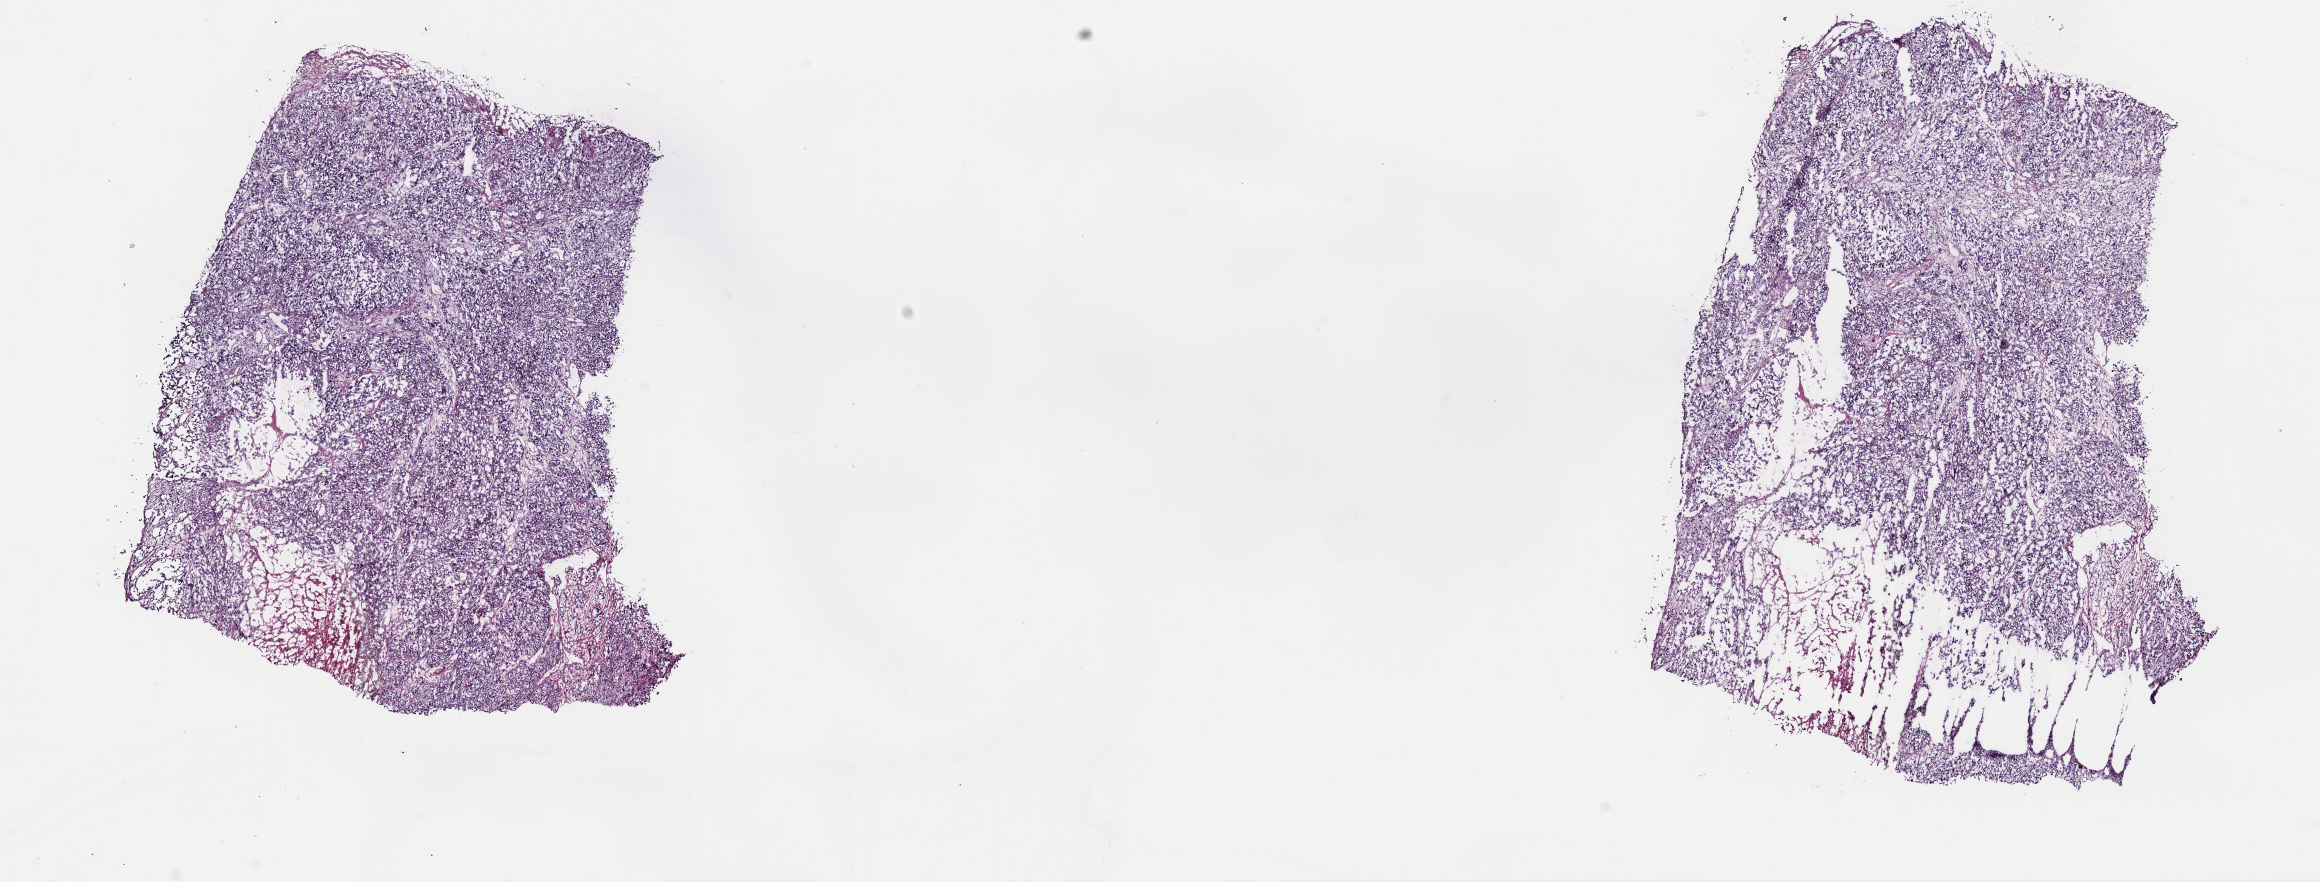
Whole-slide histology image, H&E-stained — low-resolution overview of the scanned area, about 18.3 x 7.0 mm (slide scanned at 40x), frozen section from the top of the tissue portion, primary tumour sample from the skin. Female patient; age at initial diagnosis 75 years. Slide review estimates, as recorded: tumour cells 95%, tumour nuclei 92%, normal cells 0%, stromal cells 0%, necrosis 5%. Inflammatory infiltration, as recorded: lymphocyte infiltration 0%, monocyte infiltration 0%, neutrophil infiltration 0%.
Pathologic diagnosis: Malignant melanoma, NOS. AJCC pathologic stage: IIIC.